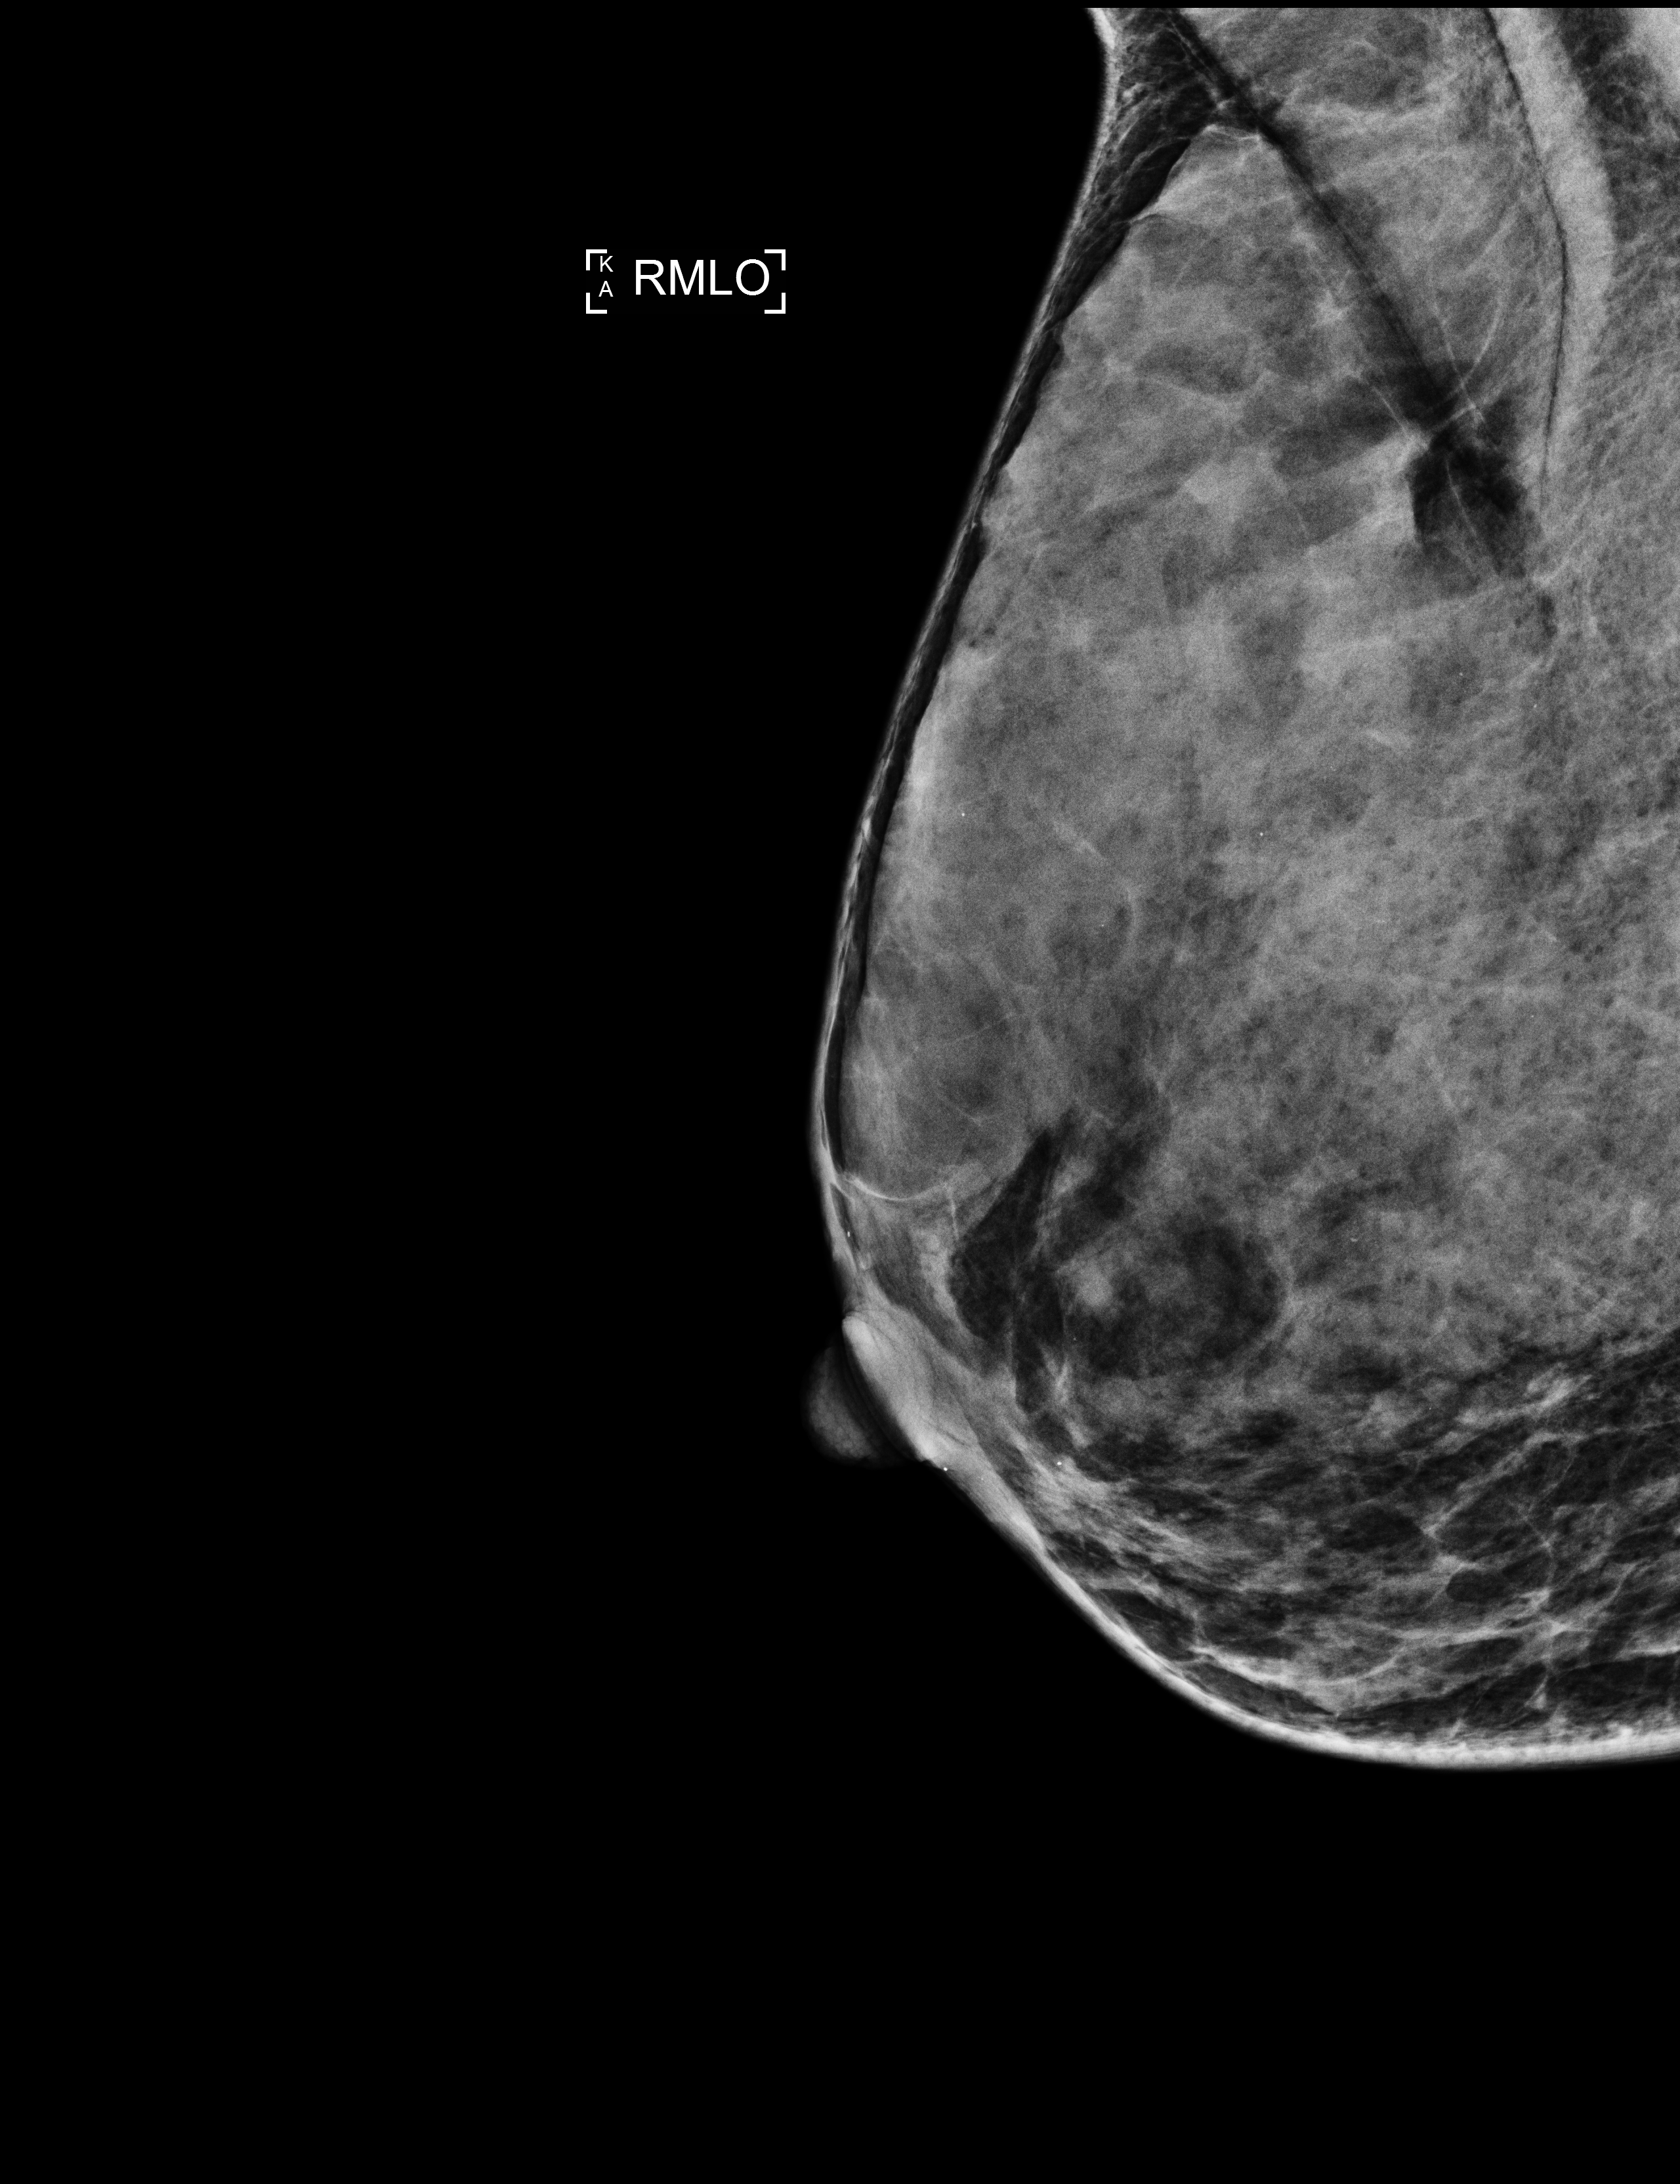
Digital mammogram (FFDM), right breast, MLO view, screening examination, compressed breast thickness 38 mm. Patient aged 41 years (female).
BI-RADS breast density category at the screening exam (both breasts, scale 1–4): 4. Final BI-RADS assessment for this screening round (tomosynthesis exam, both breasts): category 2. Recall: no recall after this screen.